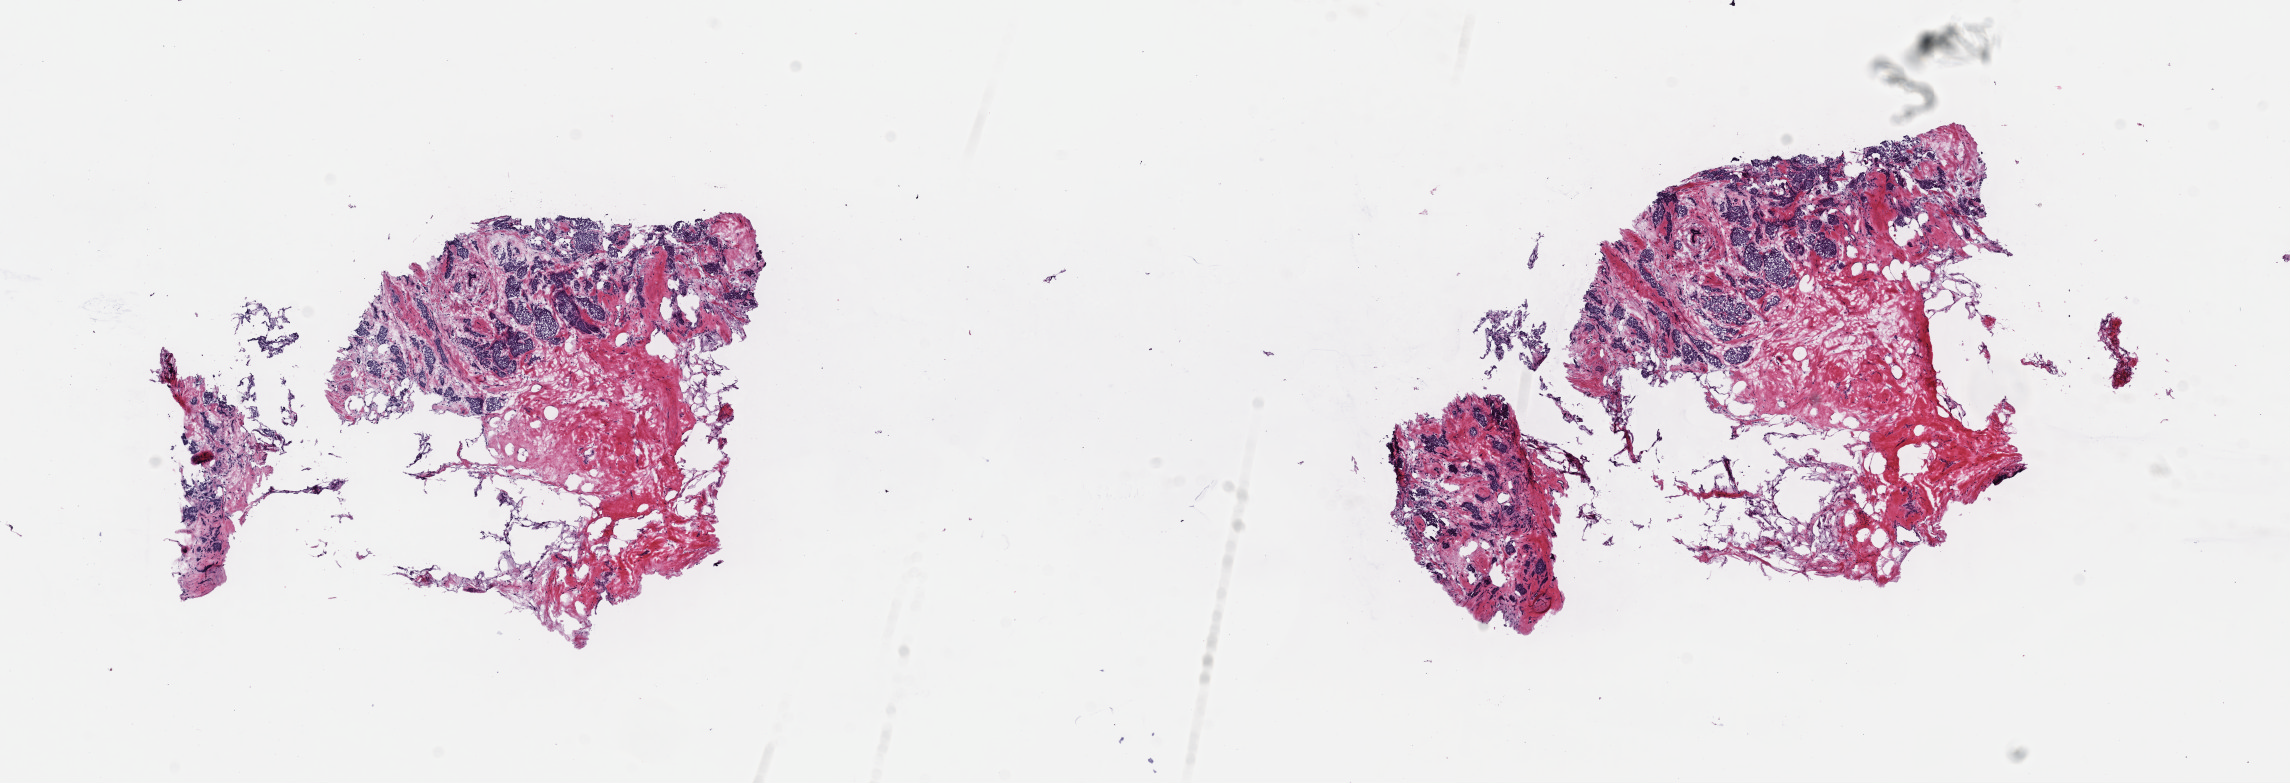
Whole-slide histology image, Hematoxylin and eosin (H&E) stained — whole scanned area (about 18.1 x 6.2 mm, acquisition: 40x scan) shown as a low-resolution overview; frozen section from the top of the tissue portion; sample: primary tumour, breast. Patient: female, age at initial diagnosis 63 years. Pathologist review of this section (percent, as recorded): tumour cells 55%, tumour nuclei 75%, normal cells 0%, stromal cells 45%, necrosis 0%. Infiltration values recorded for this section: lymphocyte infiltration 0%, monocyte infiltration 0%, neutrophil infiltration 0%.
AJCC pathologic stage: IIA. Histologic diagnosis: Infiltrating duct carcinoma, NOS.